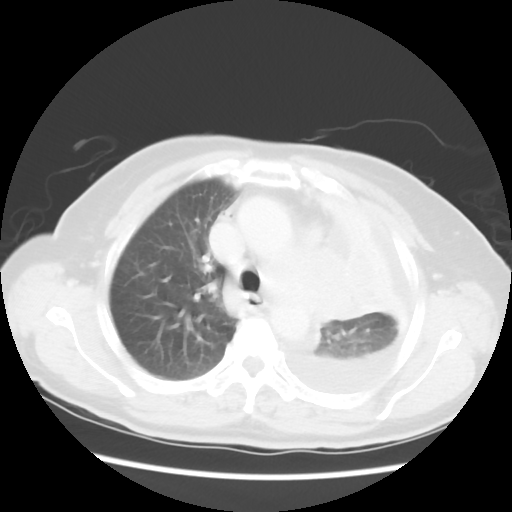
Chest CT, one axial slice; position 38 of 52 along the scan axis; reconstruction kernel STANDARD; 120 kVp; lung window (W 1500 / L -600 HU); 5 mm slice thickness; 512 × 512 image matrix. Female patient, age 72 years. Case-level facts recorded for this patient, not image findings: clinical TNM (as recorded): T4 N3 M1b.
Structures marked on this image (bounding box drawn by a radiologist):
- lung tumour (recorded histology: large cell carcinoma): bounding box <290,241,387,325> (left, top, right, bottom; pixels)